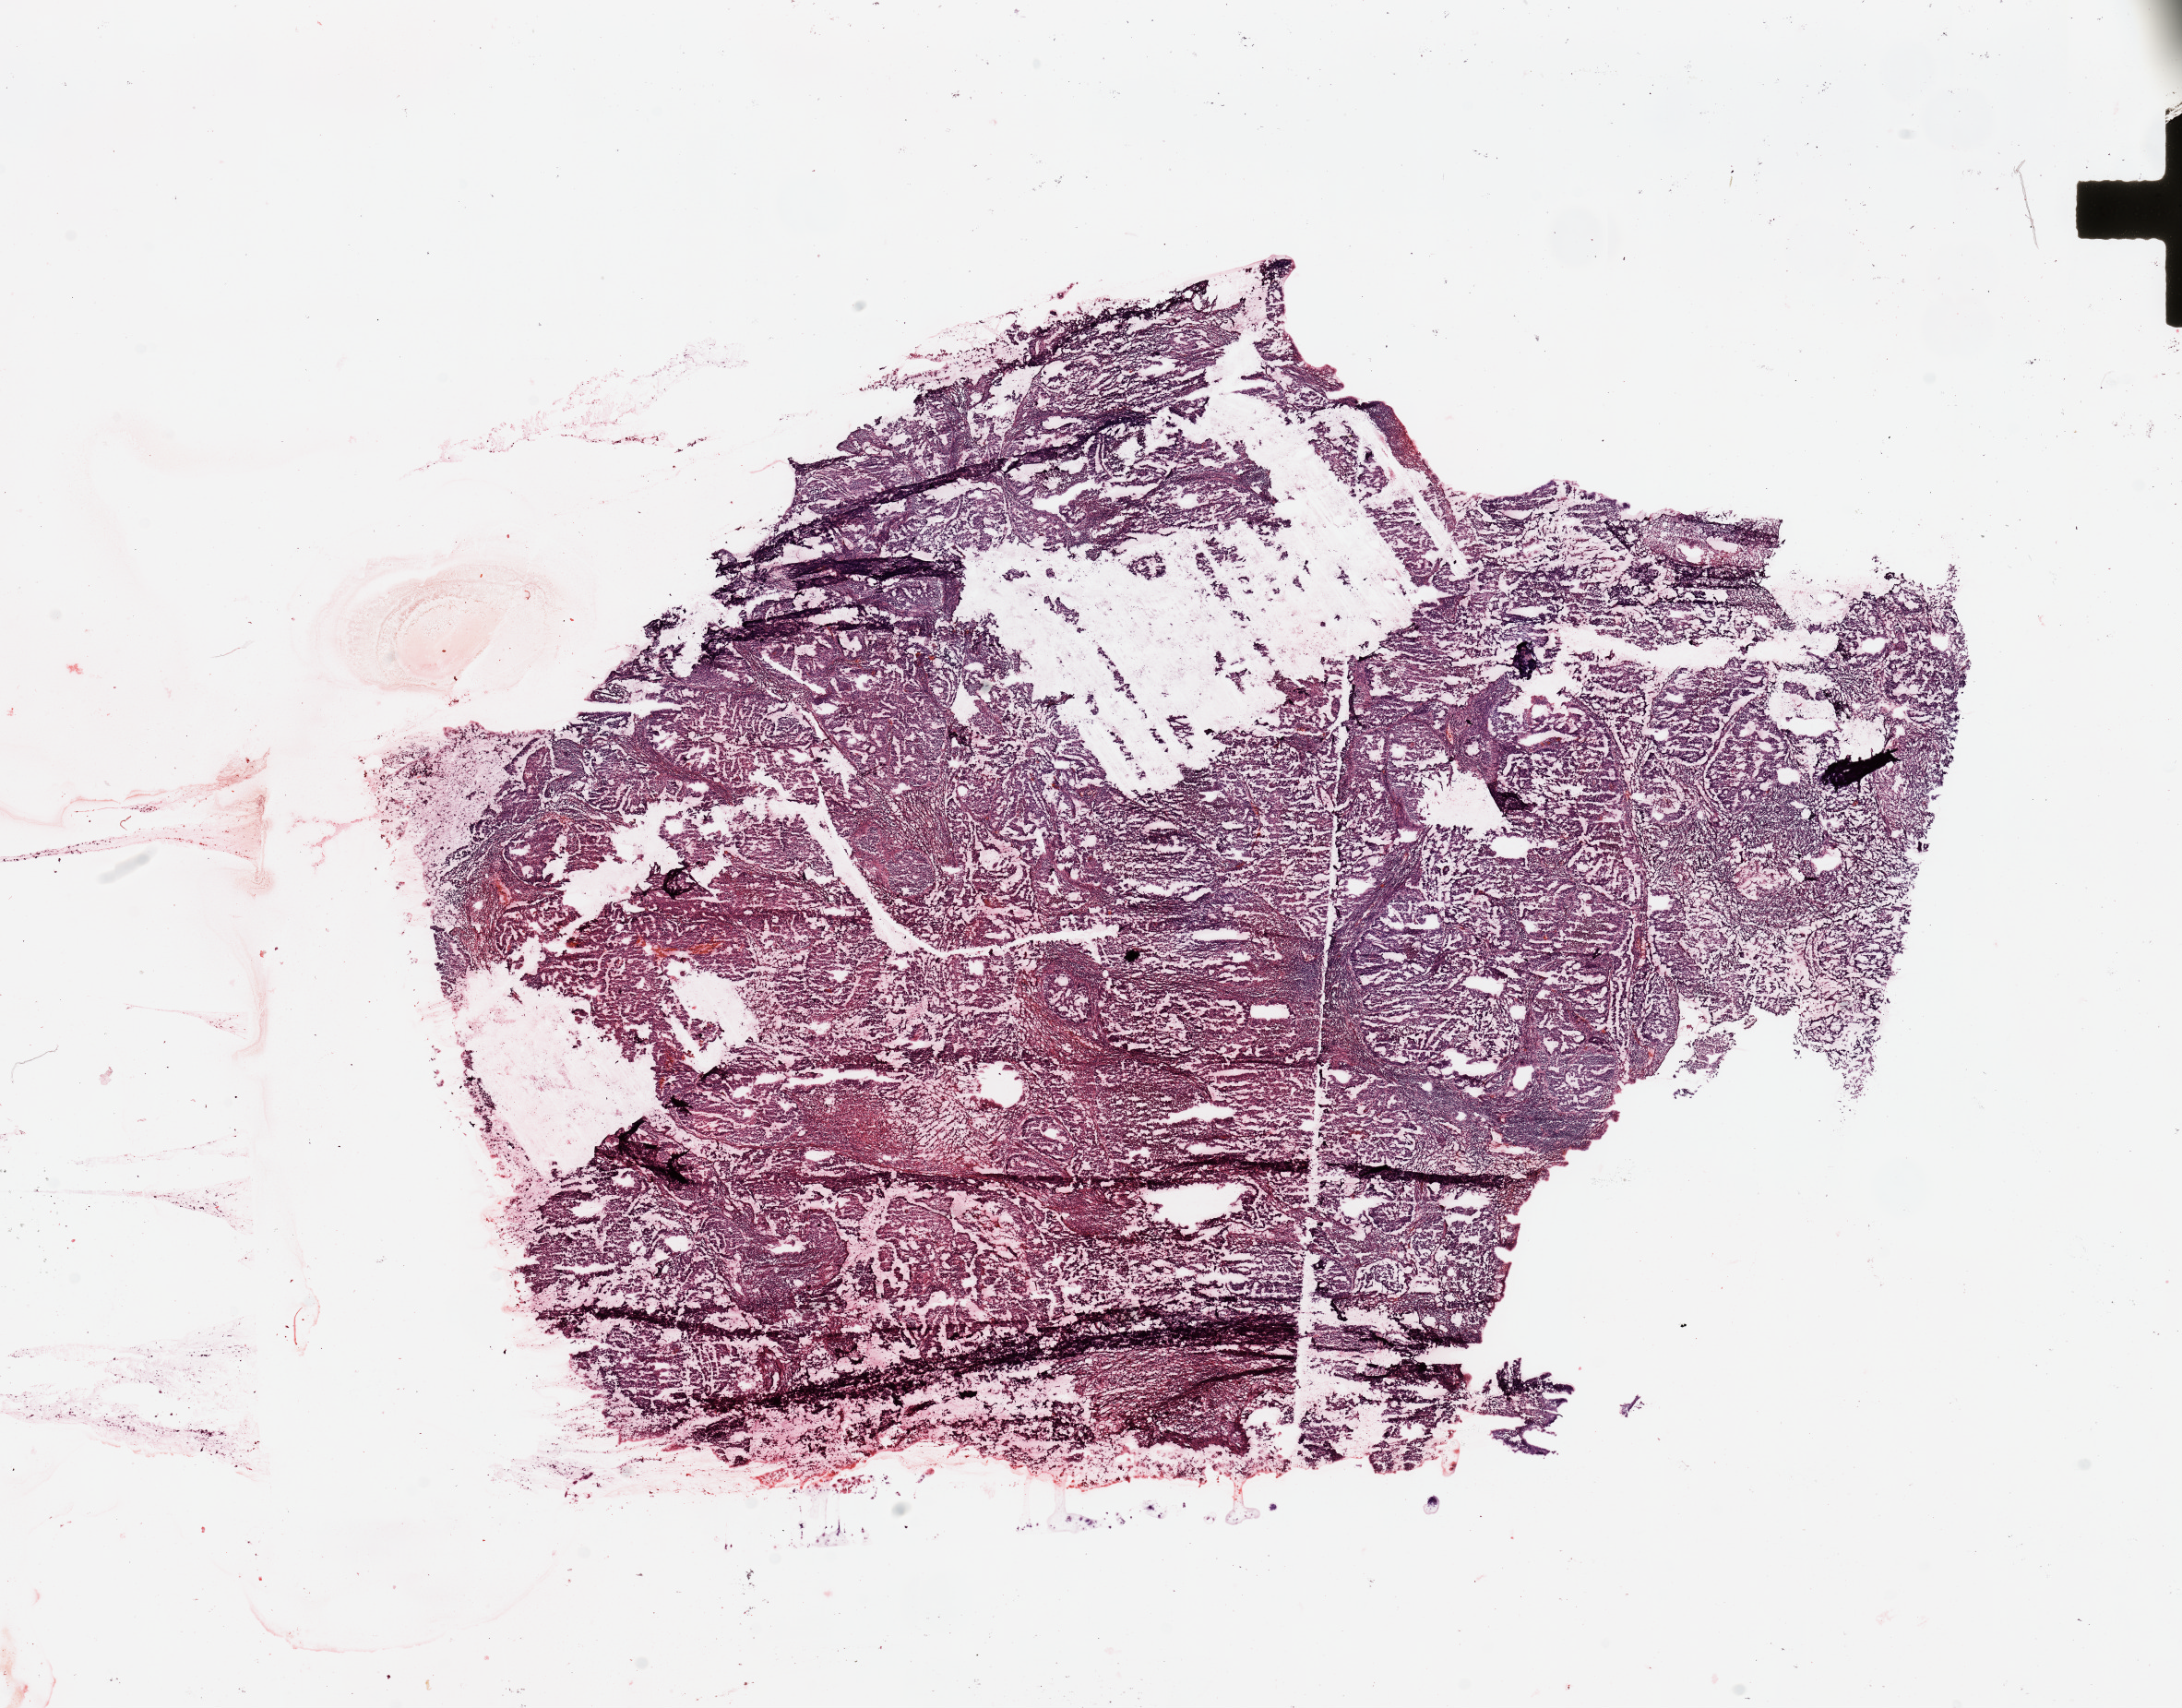
Whole-slide histology image, H&E — a low-resolution overview of the entire scanned area, about 18.7 x 14.6 mm (acquisition: 20x scan); tumour tissue sample, sampled site: uterus. Patient: female, age 45 years. Slide review estimates, as recorded: tumour nuclei 90%, necrosis 0%.
Diagnosis: Endometrioid adenocarcinoma, NOS.